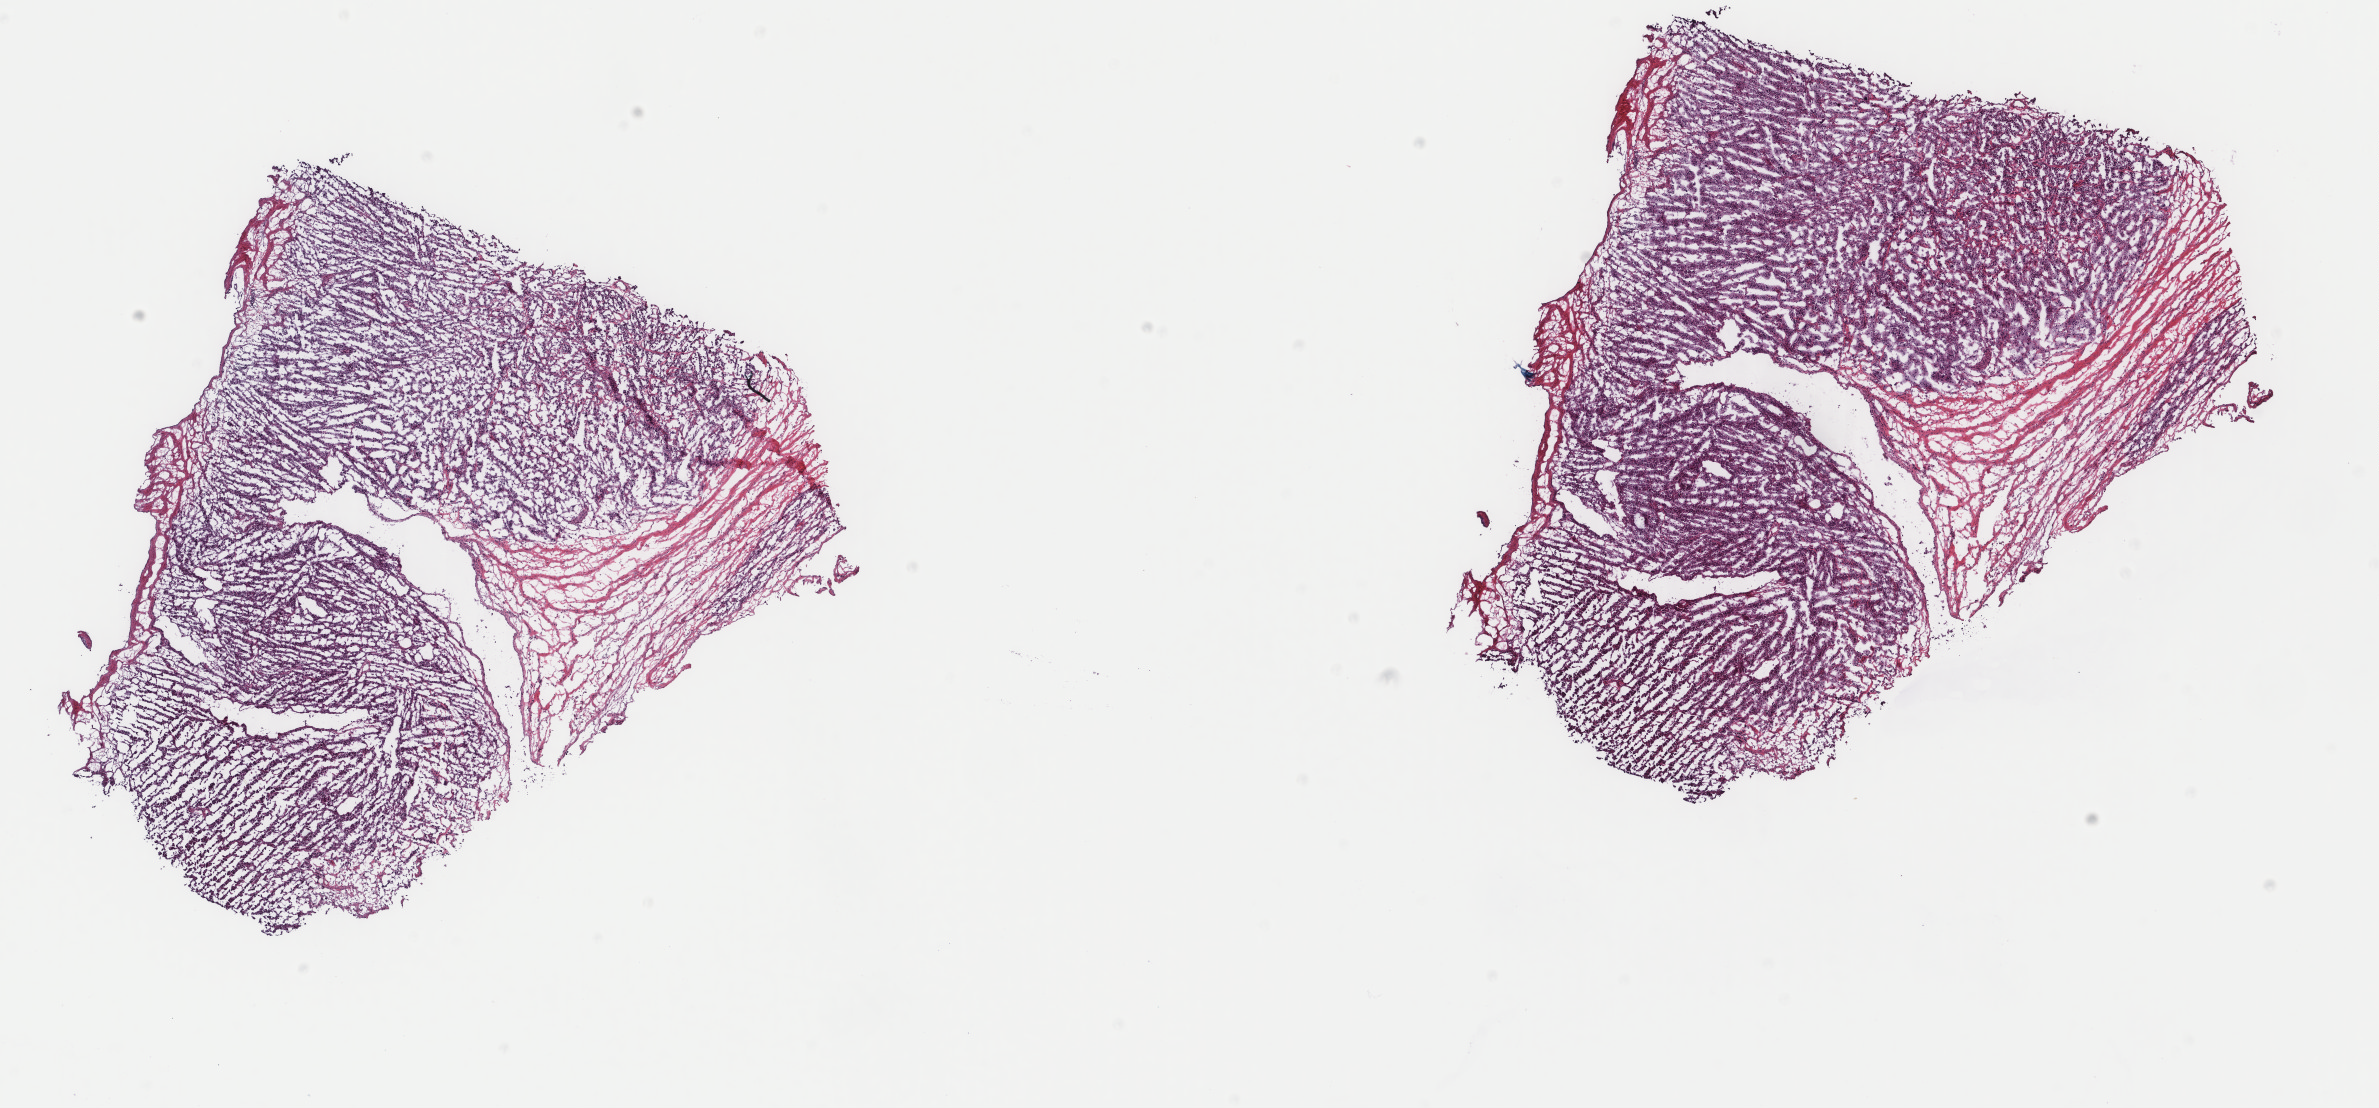
Digitized H&E tissue section (whole slide), low-resolution overview of the scanned area, about 18.9 x 8.8 mm (from a 40x scan), frozen section from the top of the tissue portion, primary tumour sample from the uterus. Female patient; age at initial diagnosis 73 years. Pathologist review of this section (percent, as recorded): tumour cells 80%, tumour nuclei 85%.
Histologic diagnosis: Leiomyosarcoma, NOS.